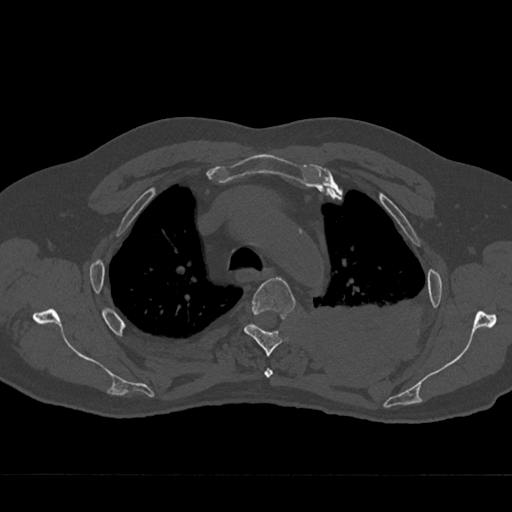
CT including the spine, one axial slice; slice 522 of 797 in the series (ordered by position); 120 kVp; bone window (W 1800 / L 400 HU); 512 × 512 image matrix, field of view 377 × 377 mm. Patient: male, 75 years. From the clinical record (not read from this slice): primary cancer: renal; vertebrae with lytic lesions (as recorded): T4.
Annotated regions visible in this slice (semi-automatic segmentation, software-assisted and operator-edited):
- T3 vertebra: bounding box [x1, y1, x2, y2] px = [264, 368, 273, 378]
- T4 vertebra: [244, 277, 296, 356]